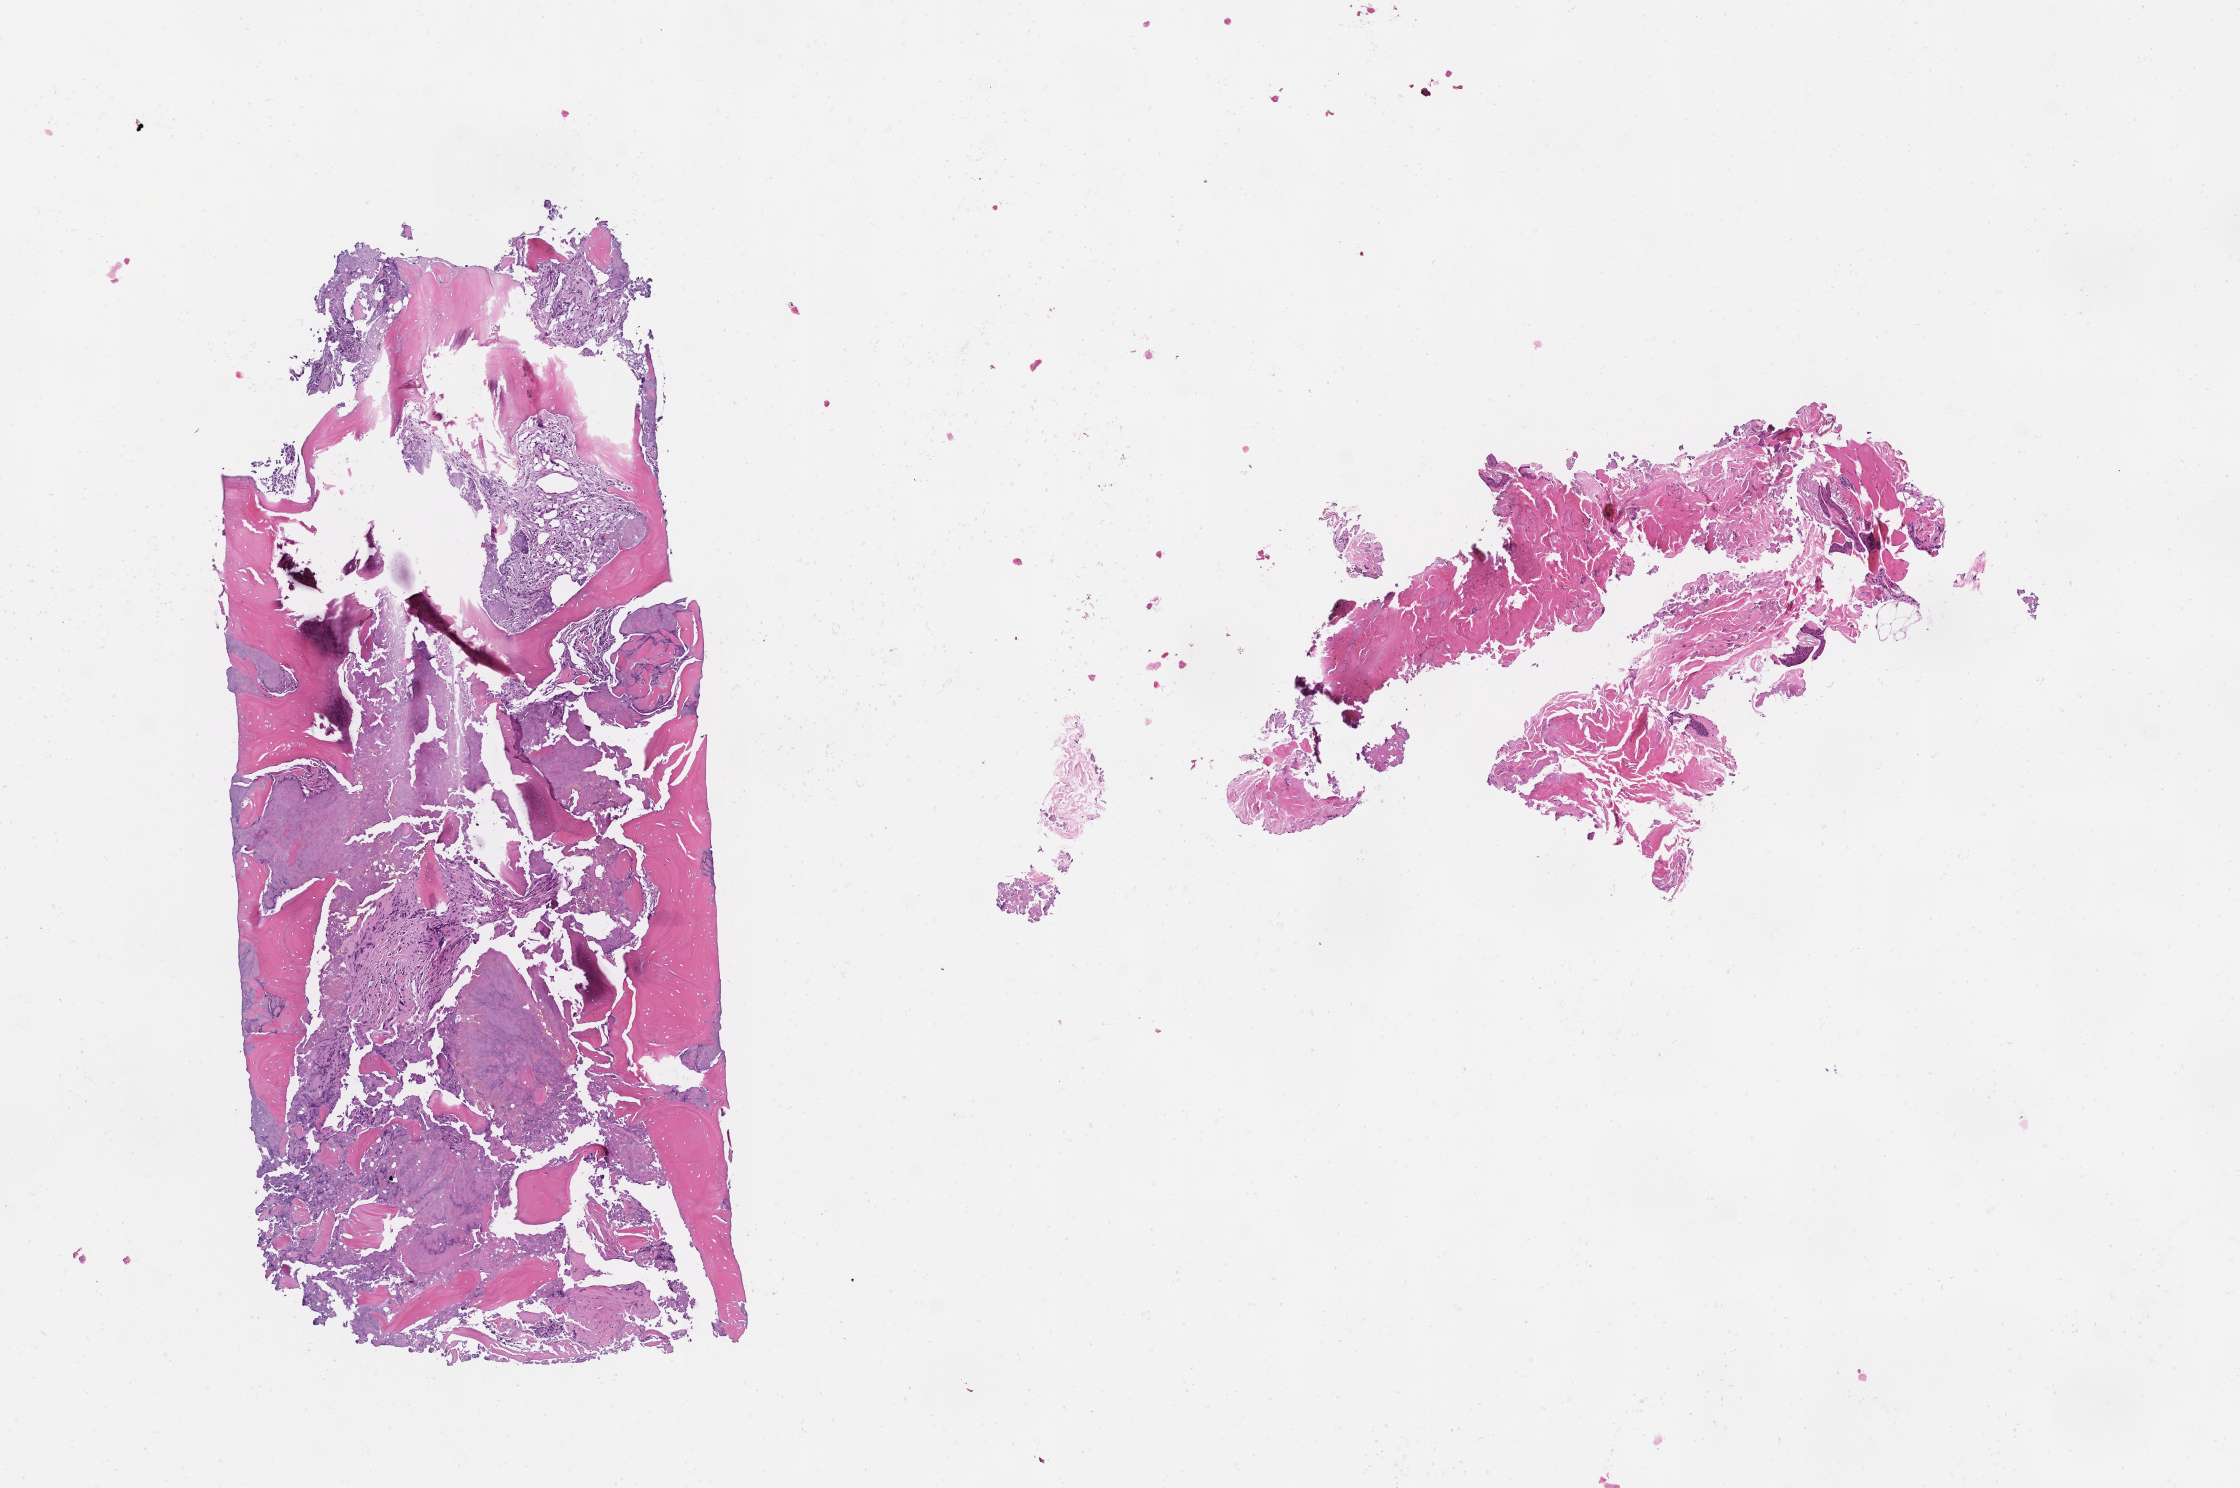
Whole-slide image, haematoxylin and eosin stain, low-resolution overview of the scanned area, about 9.0 x 6.0 mm. FFPE section. Archival tissue. Patient: female.
This section: metastasis (sampled organ not recorded). Primary diagnosis of the patient: Invasive Breast Carcinoma.